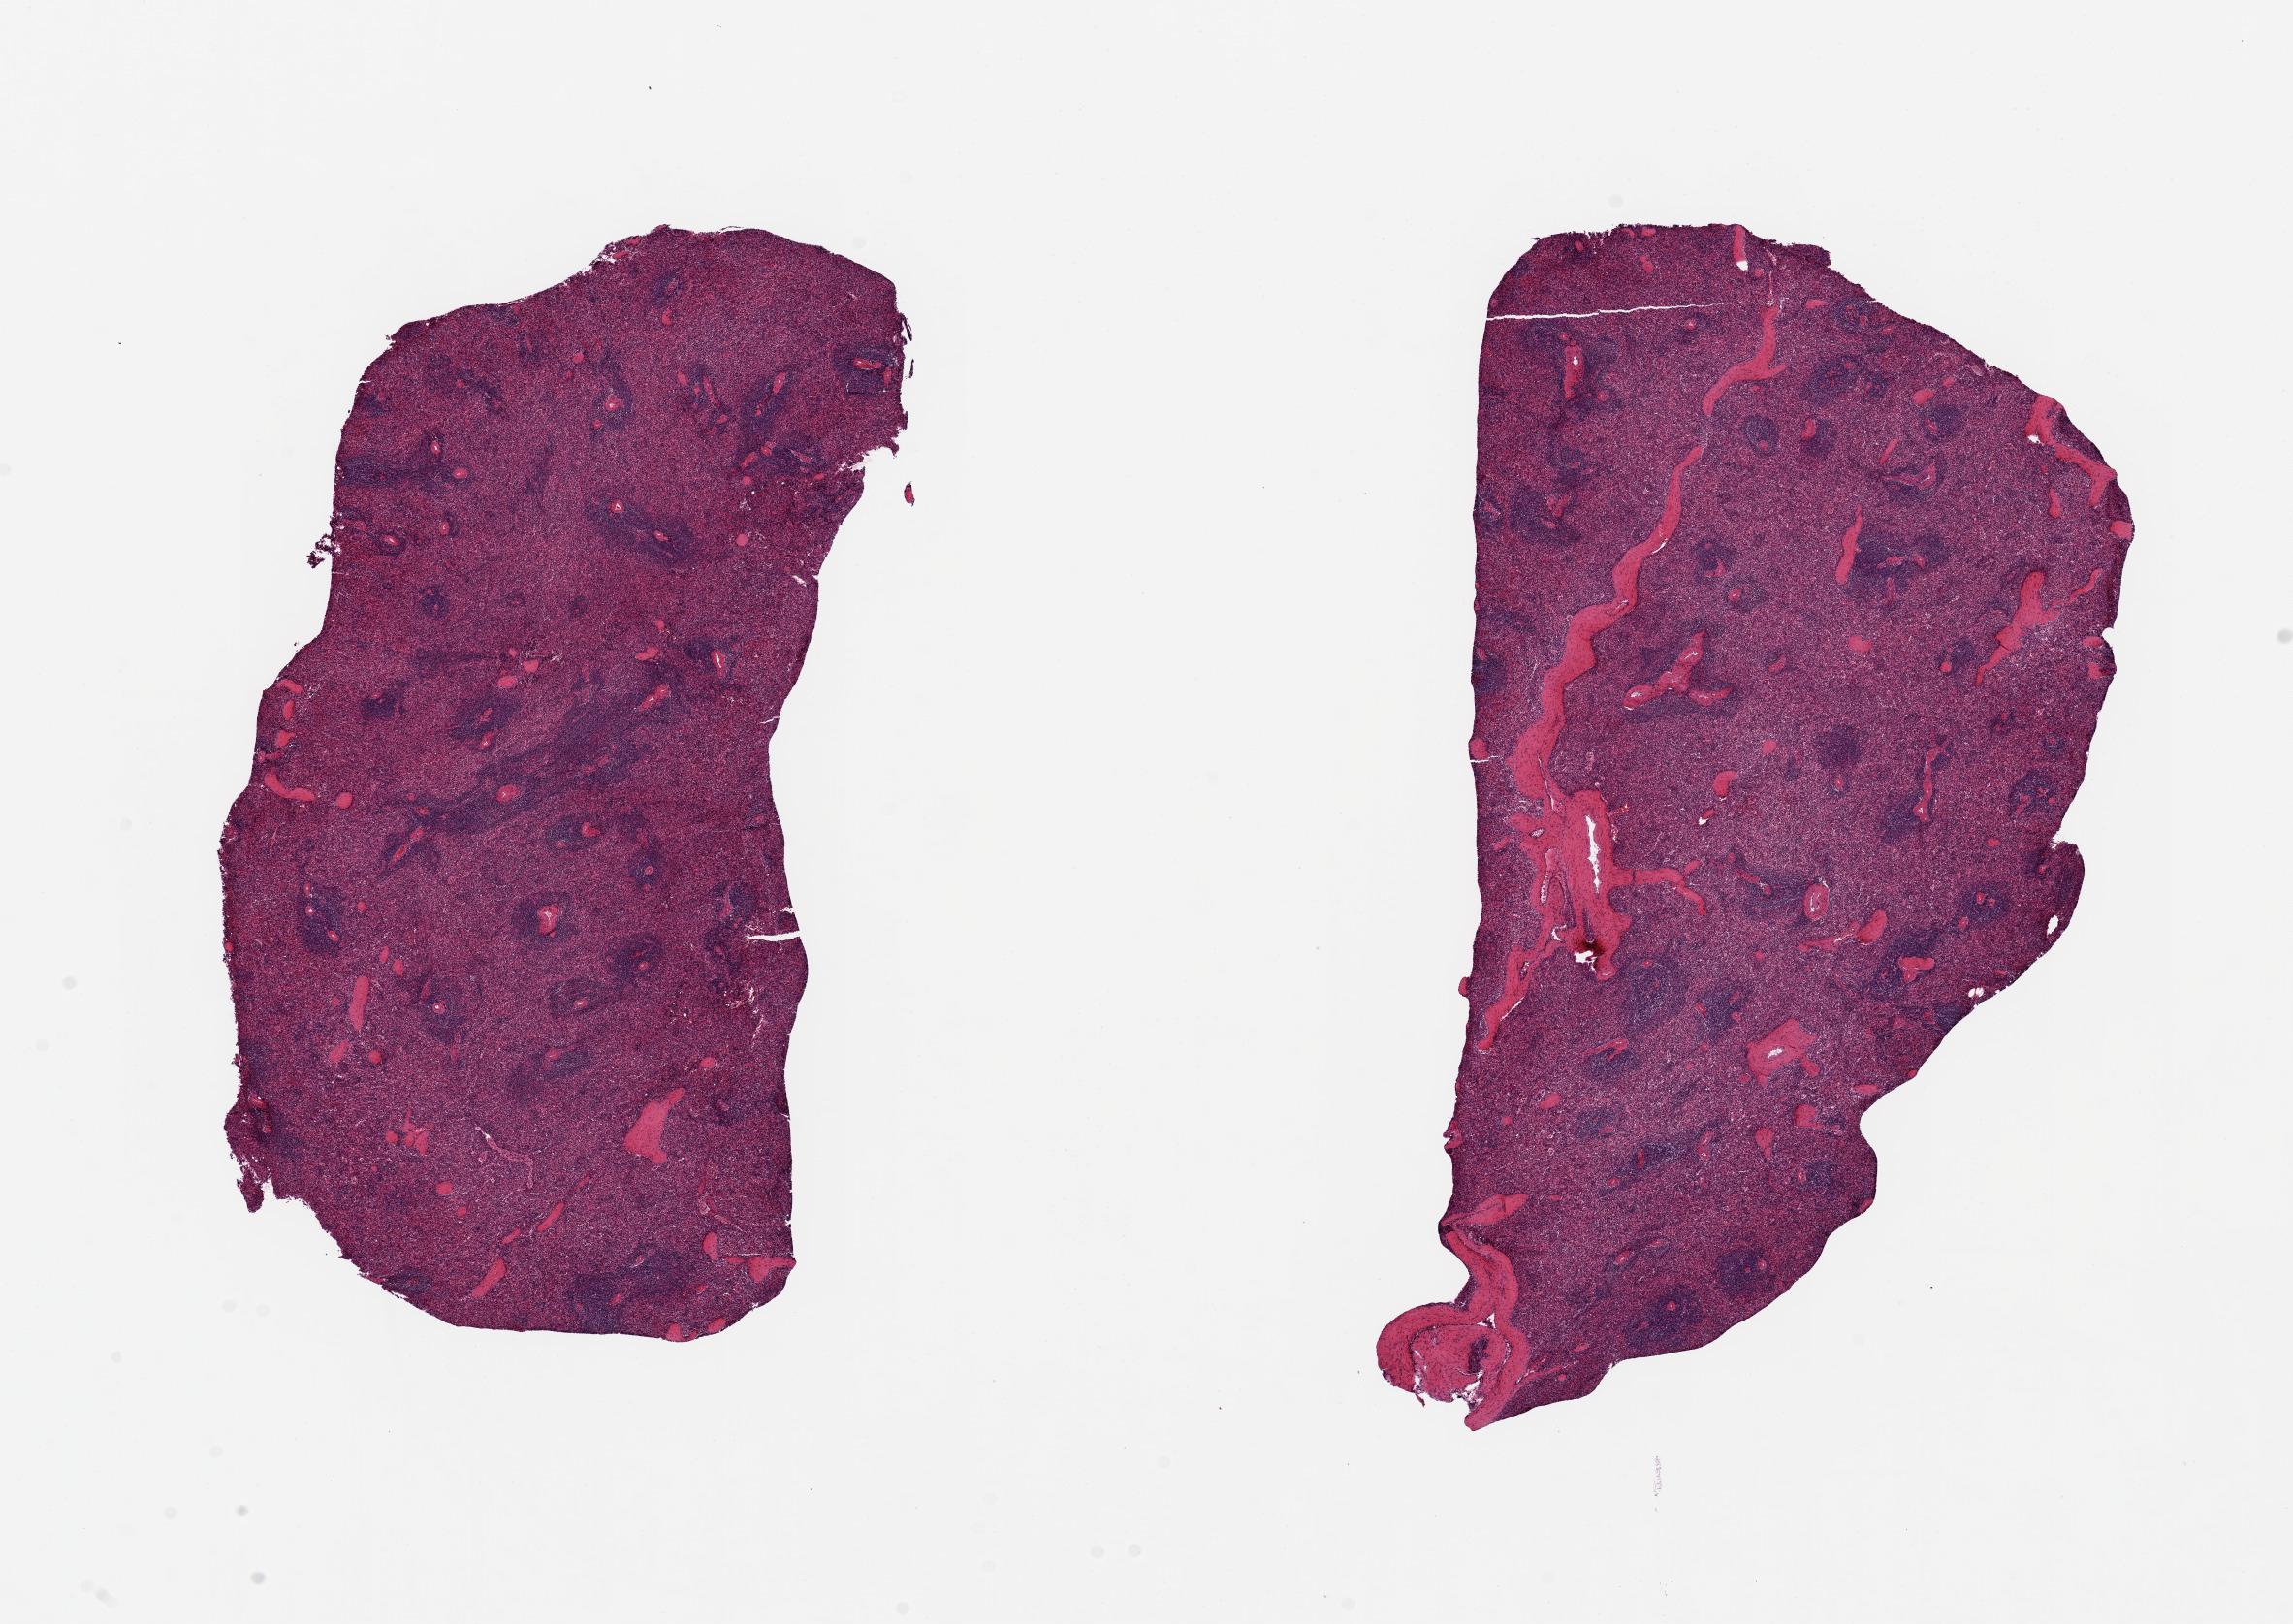
Haematoxylin and eosin whole-slide image, brightfield — whole scanned area (about 18.7 x 13.2 mm, acquisition: 20x scan) shown as a low-resolution overview; PAXgene-fixed, paraffin-embedded tissue; target tissue: spleen; donor tissue sample. Female donor.
Review note (as recorded): 2 ~9x5mm pieces.